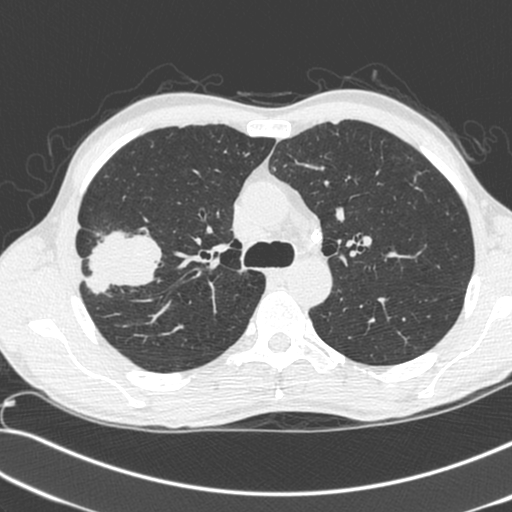
Low-dose screening chest CT, axial slice, baseline screening round, lung window (W 1500 / L -600 HU), 1.3 mm slice thickness, slice 79 of 281 in the series, 512 × 512 image matrix. Male, age 55 years at enrolment. Current smoker at enrolment.
Expert-annotated lung lesion, bounding box (x1, y1, x2, y2) in pixels: (70, 230, 152, 304). Reader record for this screening exam (exam-level; its link to the box is not recorded): non-calcified nodule or mass ≥4 mm, right upper lobe, 52 × 39 mm, spiculated (stellate) margins, soft tissue attenuation. Lung cancer was diagnosed 25 days after this screen: large cell neuroendocrine carcinoma, right upper lobe, poorly differentiated (G3), stage IIB (AJCC 6th edition), 49 mm at pathology.